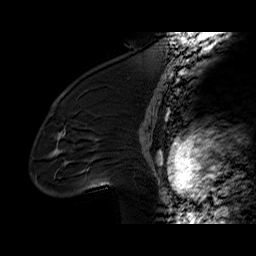
Breast MRI (dynamic contrast-enhanced), one sagittal slice. Slice 41 of 60 in the series (ordered by position). Dynamic contrast-enhanced series, time point 2 of 6 at this slice position (early post-contrast). 1.5 T. TE 6.2 ms, TR 32.4 ms. 4 mm slice thickness. 256 × 256 image matrix, field of view 200 × 200 mm. Female patient. From the clinical record (not read from this slice): setting: breast cancer imaged before/during neoadjuvant chemotherapy; receptor status: triple-negative.
Outlined on this slice (semi-automatic segmentation, software-assisted and operator-edited):
- analysis volume of interest (the breast-tissue region the enhancement analysis was run in; not a lesion): box from (x=36, y=97) to (x=134, y=196) px
- tumour enhancement mask (voxels above the 100 % enhancement threshold inside the analysis volume of interest): (x=58, y=133)–(x=61, y=139)